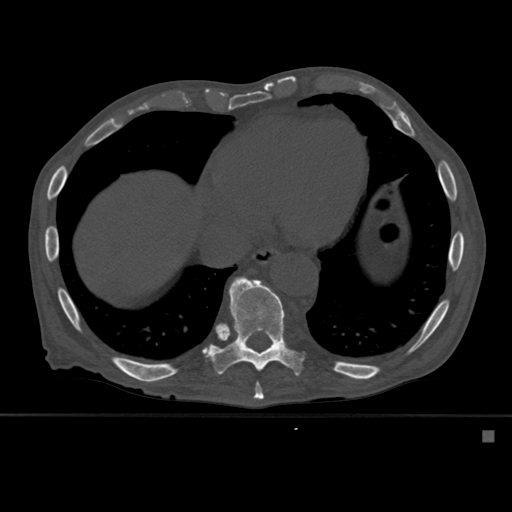
CT including the spine, one axial slice. Slice 317 of 527 in the series (ordered by position). Bone window (W 1800 / L 400 HU). 512 × 512 image matrix, field of view 373 × 373 mm. Patient: male, 78 years. Case-level facts recorded for this patient, not image findings: primary cancer: prostate.
Outlined on this slice (semi-automatically segmented with operator editing):
- T10 vertebra: bounding box (x1, y1, x2, y2) in pixels: (207, 276, 305, 376)
- T9 vertebra: (254, 382, 264, 400)